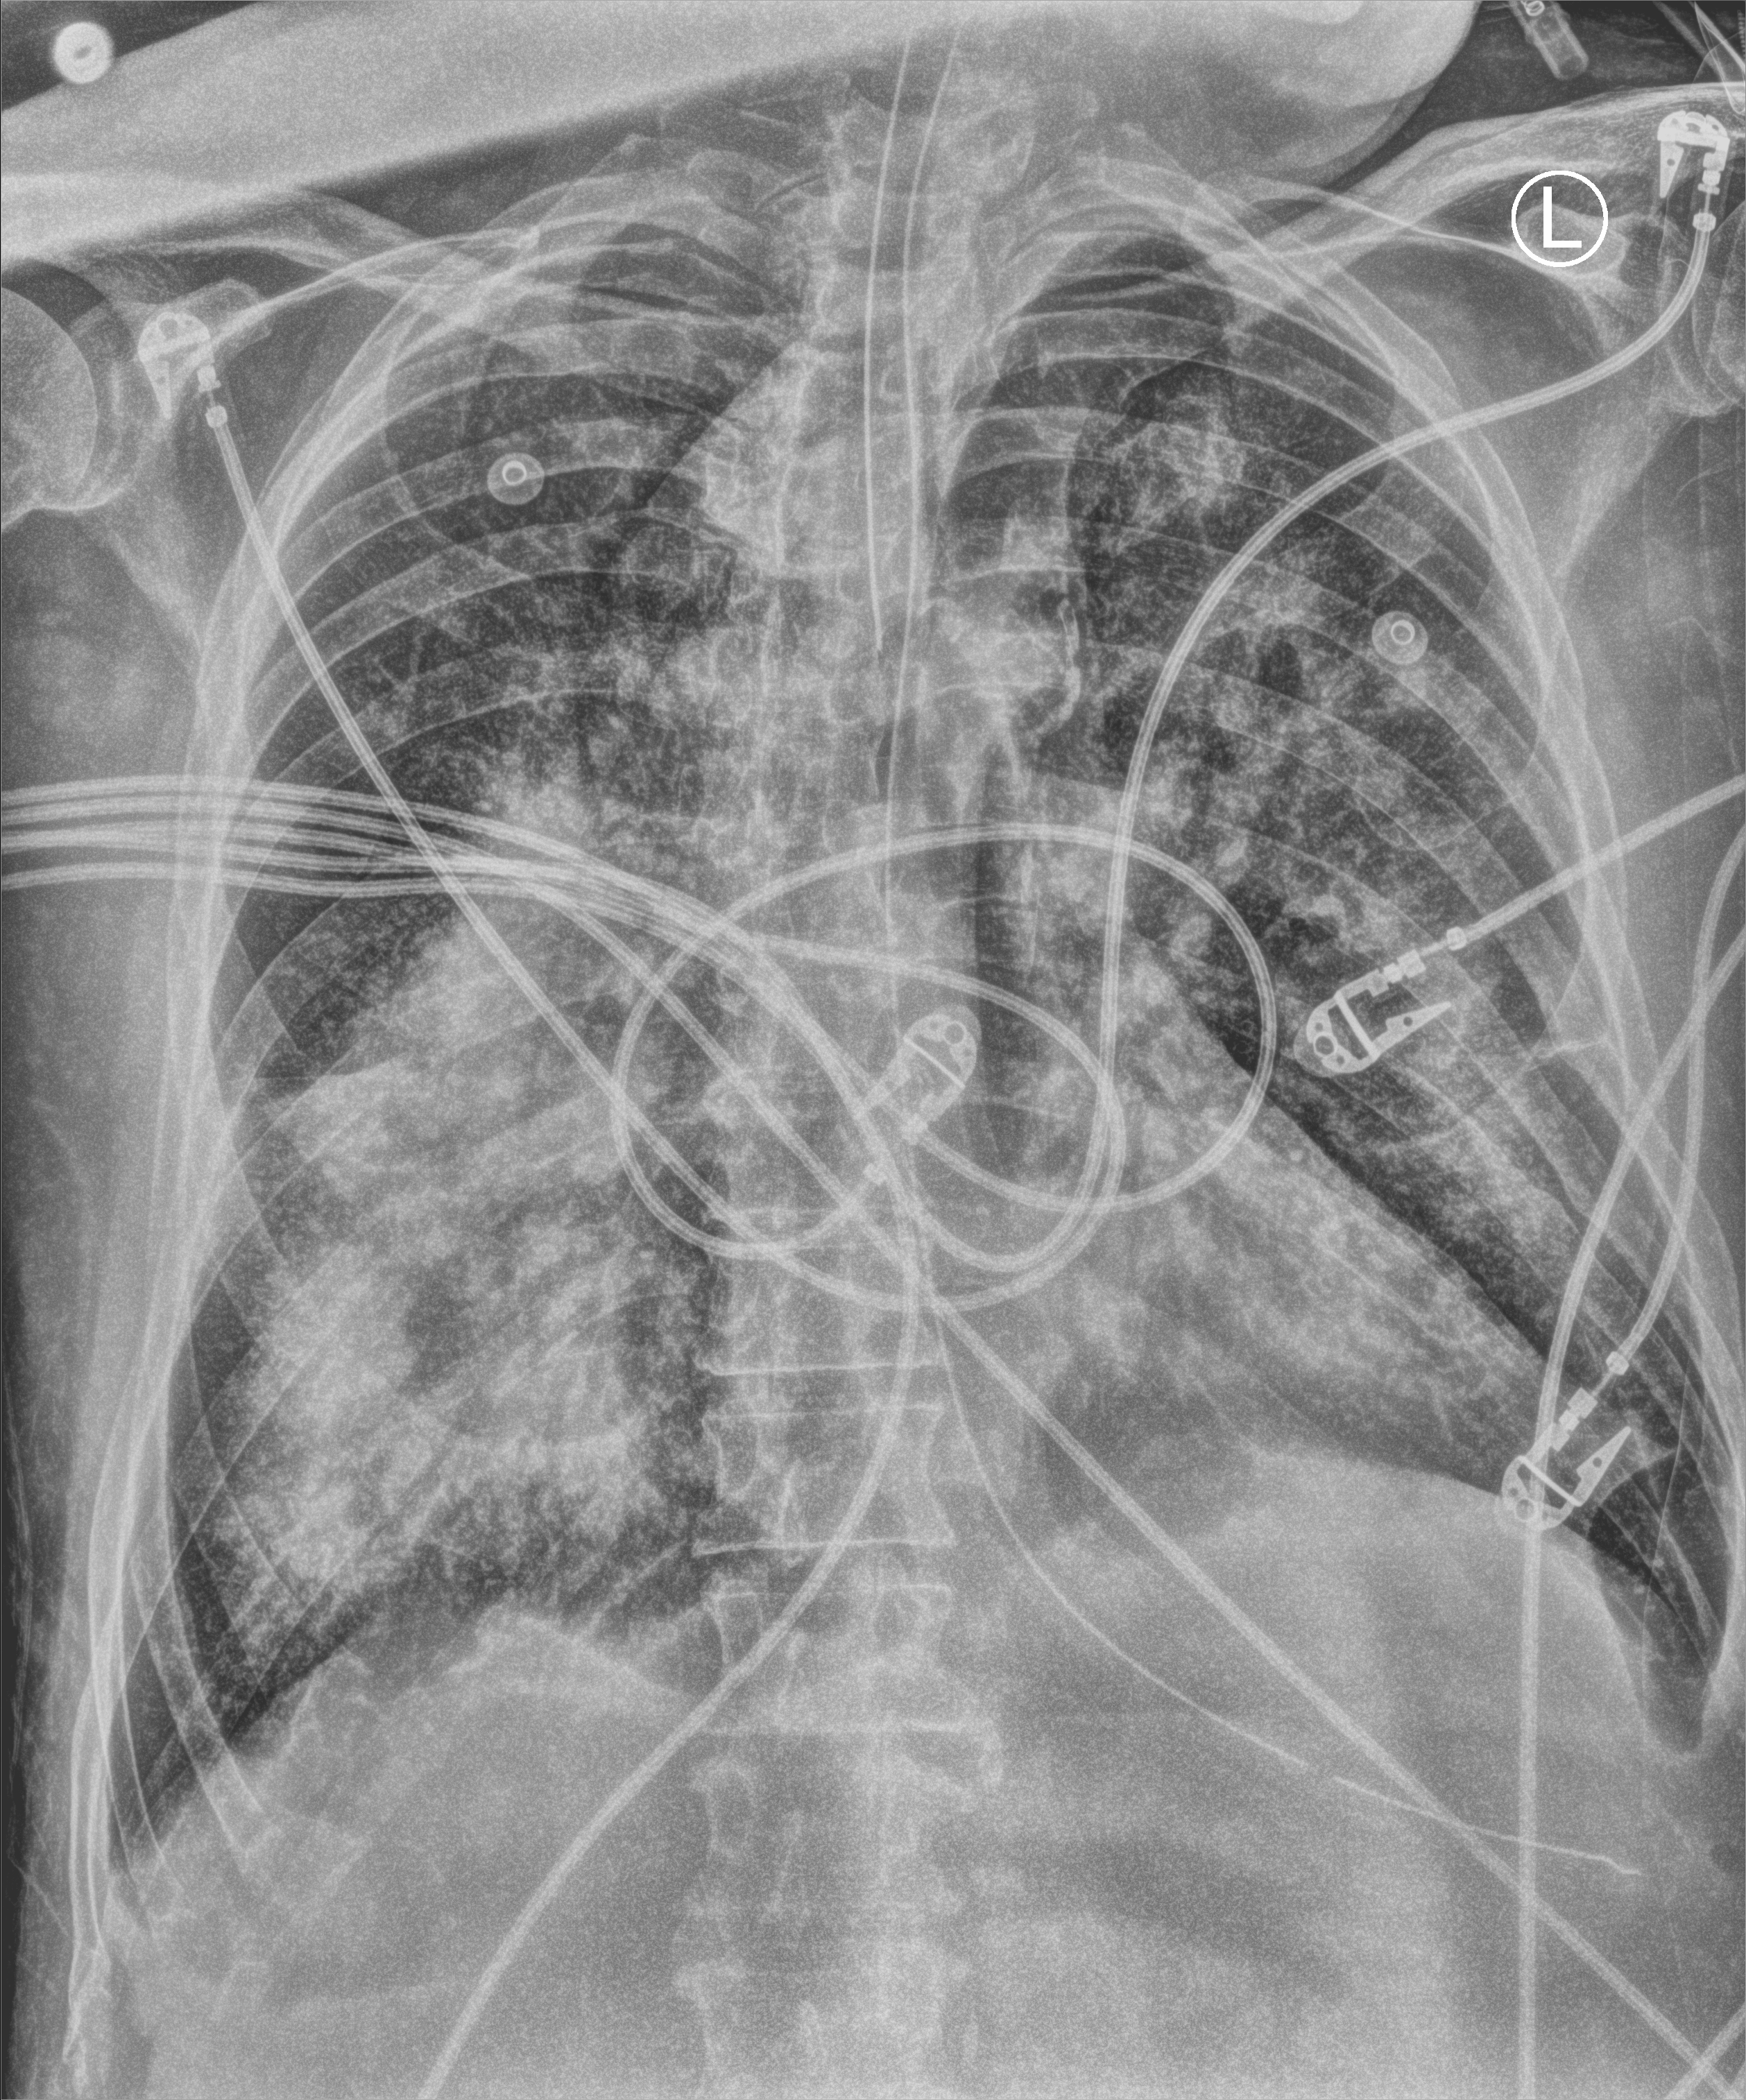
Portable chest radiograph. Patient hospitalised with COVID-19; male, aged 60–74 years.
From the hospital-stay record, not from the radiograph (when in the stay this image was taken is not recorded):
- mechanically ventilated during this hospital stay: yes
- admitted to intensive care during this hospital stay: yes